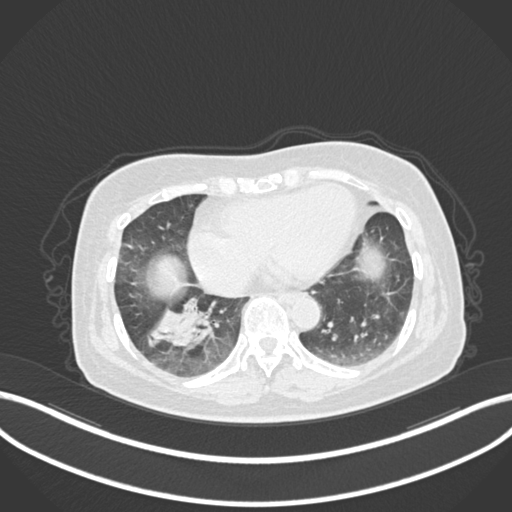
Chest CT, one axial slice; slice 39 of 222 in the series (ordered by position); 120 kVp; lung window (W 1500 / L -600 HU); 1 mm slice thickness; 512 × 512 image matrix, field of view 400 × 400 mm. Female patient, age 67 years. From the clinical record (not read from this slice): clinical TNM (as recorded): T1c N1 M0.
Structures marked on this image (rectangle marked by the reading radiologist):
- lung tumour (recorded histology: adenocarcinoma): bounding box (x1, y1, x2, y2) in pixels: (148, 294, 217, 356)